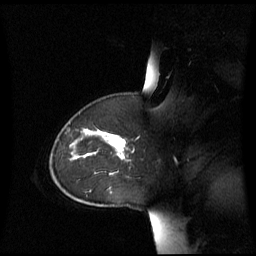
Breast MRI (dynamic contrast-enhanced), one sagittal slice. Position 46 of 60 along the scan axis. Dynamic contrast-enhanced series, image 2 of 3 at this slice position (ordered by acquisition). 1.5 T. TE 4.2 ms, TR 8.4 ms. 256 × 256 image matrix, field of view 270 × 270 mm. Female patient, age 43 years. Case-level facts recorded for this patient, not image findings: setting: breast cancer imaged before/during neoadjuvant chemotherapy; receptor status: triple-negative.
Annotated regions visible in this slice (semi-automatically segmented with operator editing):
- analysis volume of interest (the breast-tissue region the enhancement analysis was run in; not a lesion): bounding box <55,124,131,173> (left, top, right, bottom; pixels)
- tumour enhancement mask (voxels above the 70 % enhancement threshold inside the analysis volume of interest): <106,136,126,159>